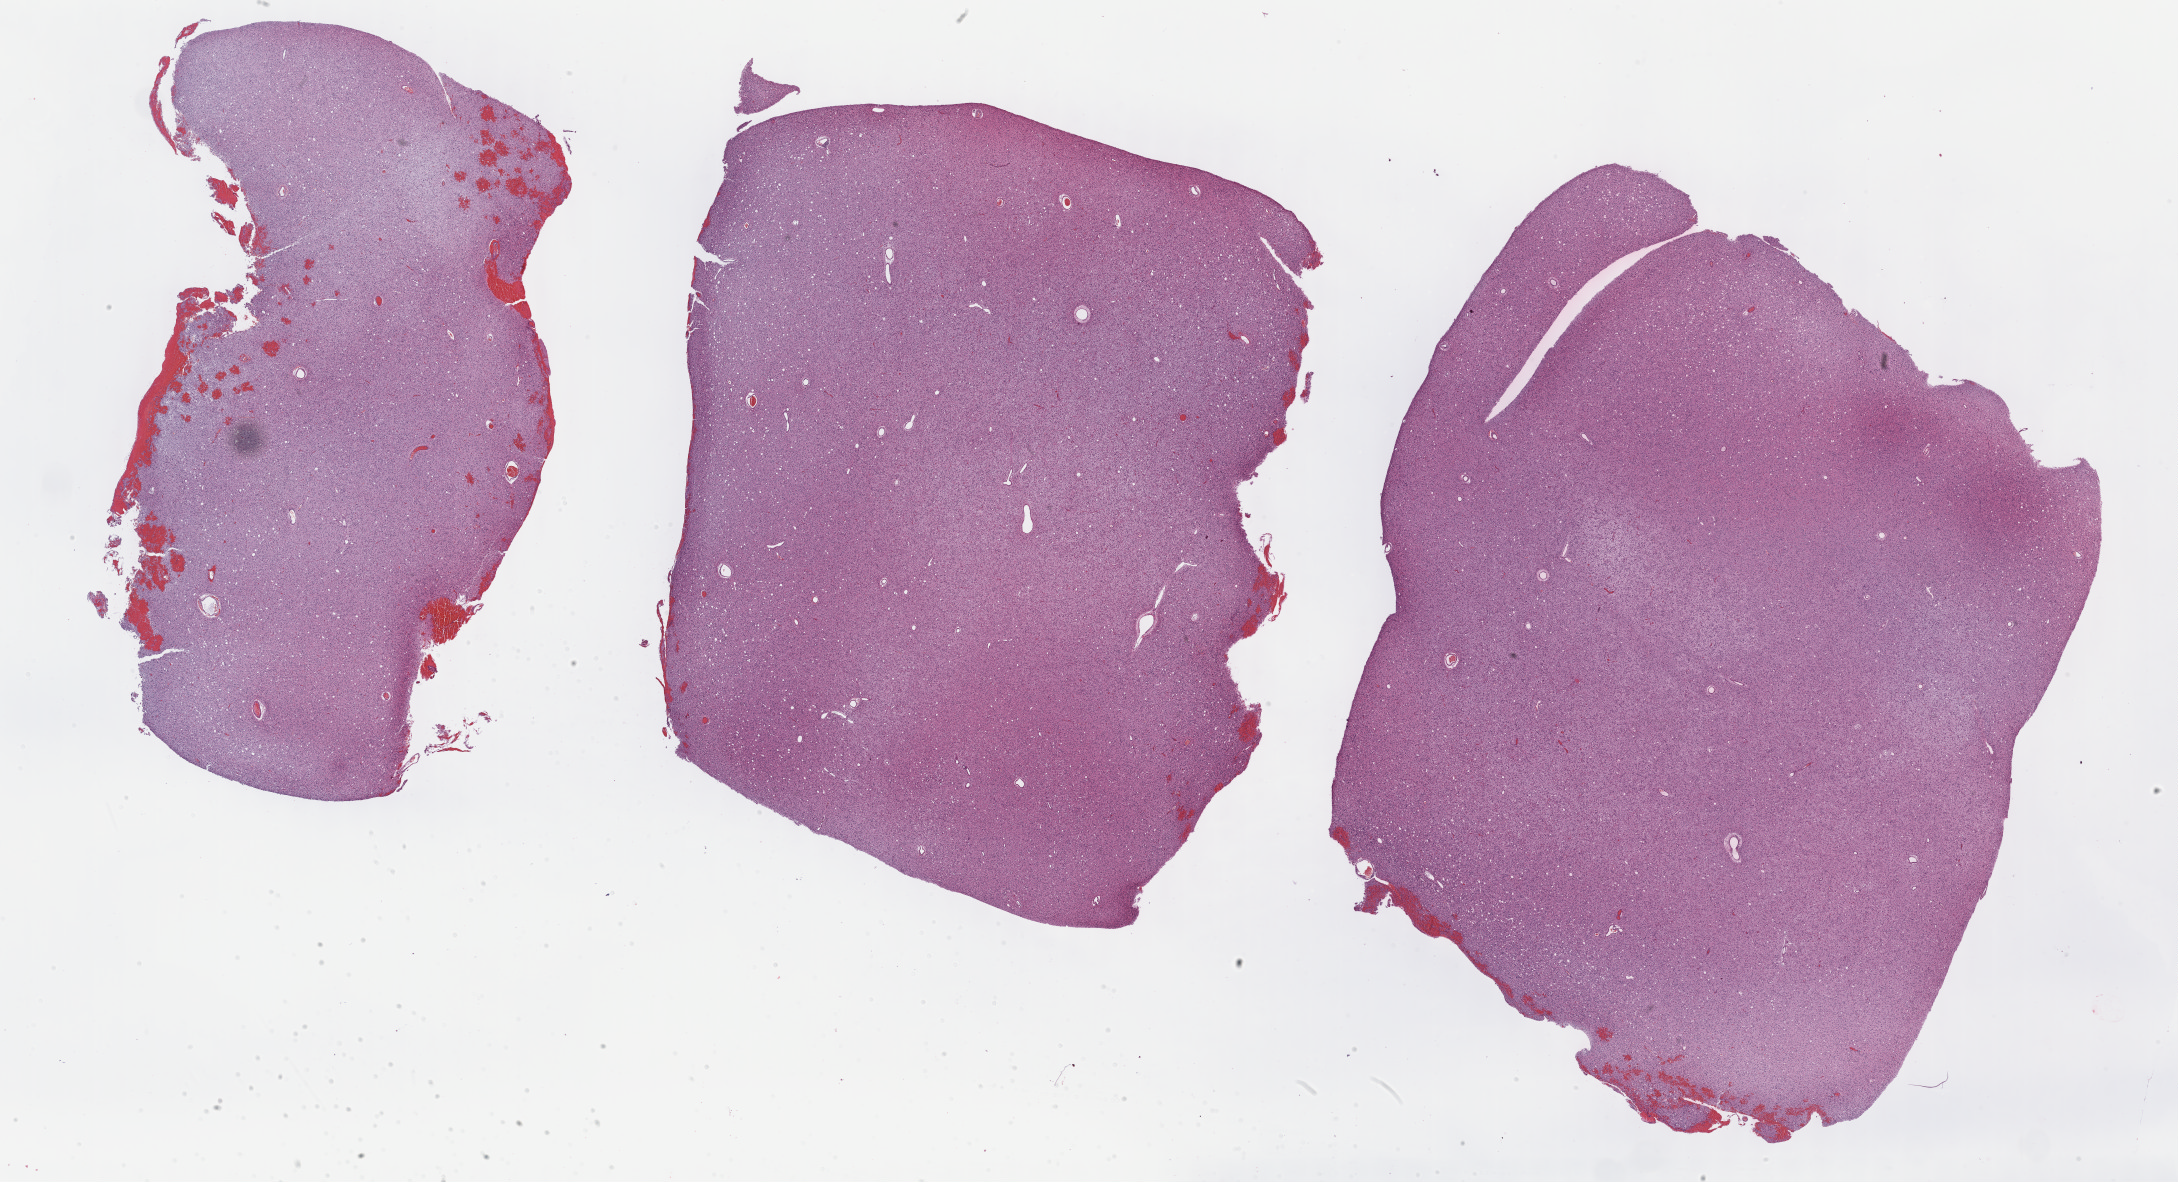
Hematoxylin and eosin (H&E) stained whole-slide image, shown as a low-resolution overview of the whole scanned area (about 35.2 x 19.1 mm, slide scanned at 40x); FFPE section; sample: primary tumour, brain. Patient: female, age at initial diagnosis 24 years. Histologic grade: G2 (moderately differentiated).
Histologic diagnosis: Astrocytoma, NOS (cerebrum). Laterality: right.